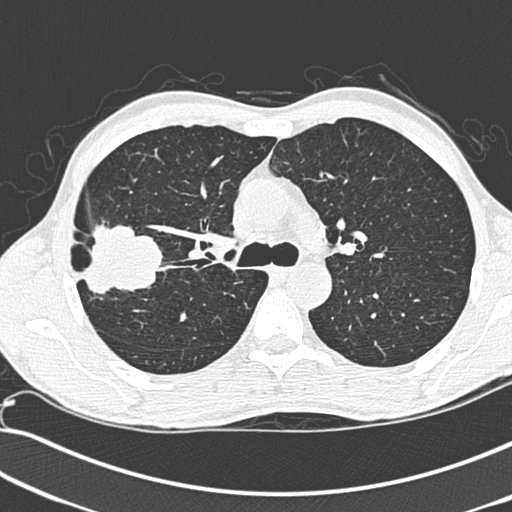
Low-dose screening chest CT, one axial slice; 120 kVp; lung window (W 1500 / L -600 HU); 512 × 512 image matrix.
Structures marked on this image (manually delineated by an expert):
- lesion 1 (tumor, upper lobe of right lung): box from (x=81, y=220) to (x=162, y=296) px